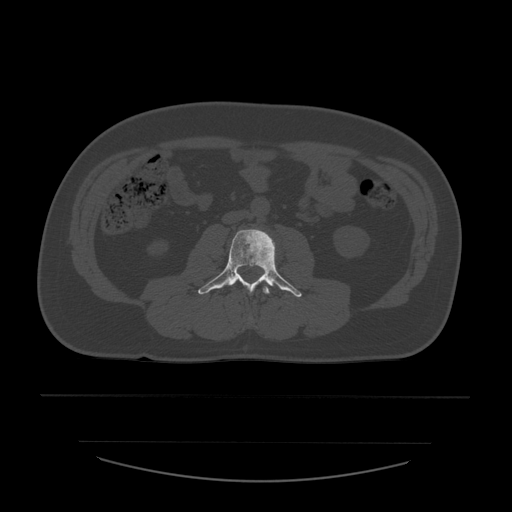
CT including the spine, one axial slice; slice 177 of 532 in the series (ordered by position); reconstruction kernel STANDARD; 120 kVp; bone window (W 1800 / L 400 HU); 1.25 mm slice thickness; 512 × 512 image matrix, field of view 441 × 441 mm. Patient age 44 years. Case-level facts recorded for this patient, not image findings: primary cancer: soft tissue sarcoma.
Annotated regions visible in this slice (semi-automatically segmented with operator editing):
- L2 vertebra: bounding box (x1, y1, x2, y2) in pixels: (249, 286, 270, 320)
- L3 vertebra: (198, 229, 302, 297)